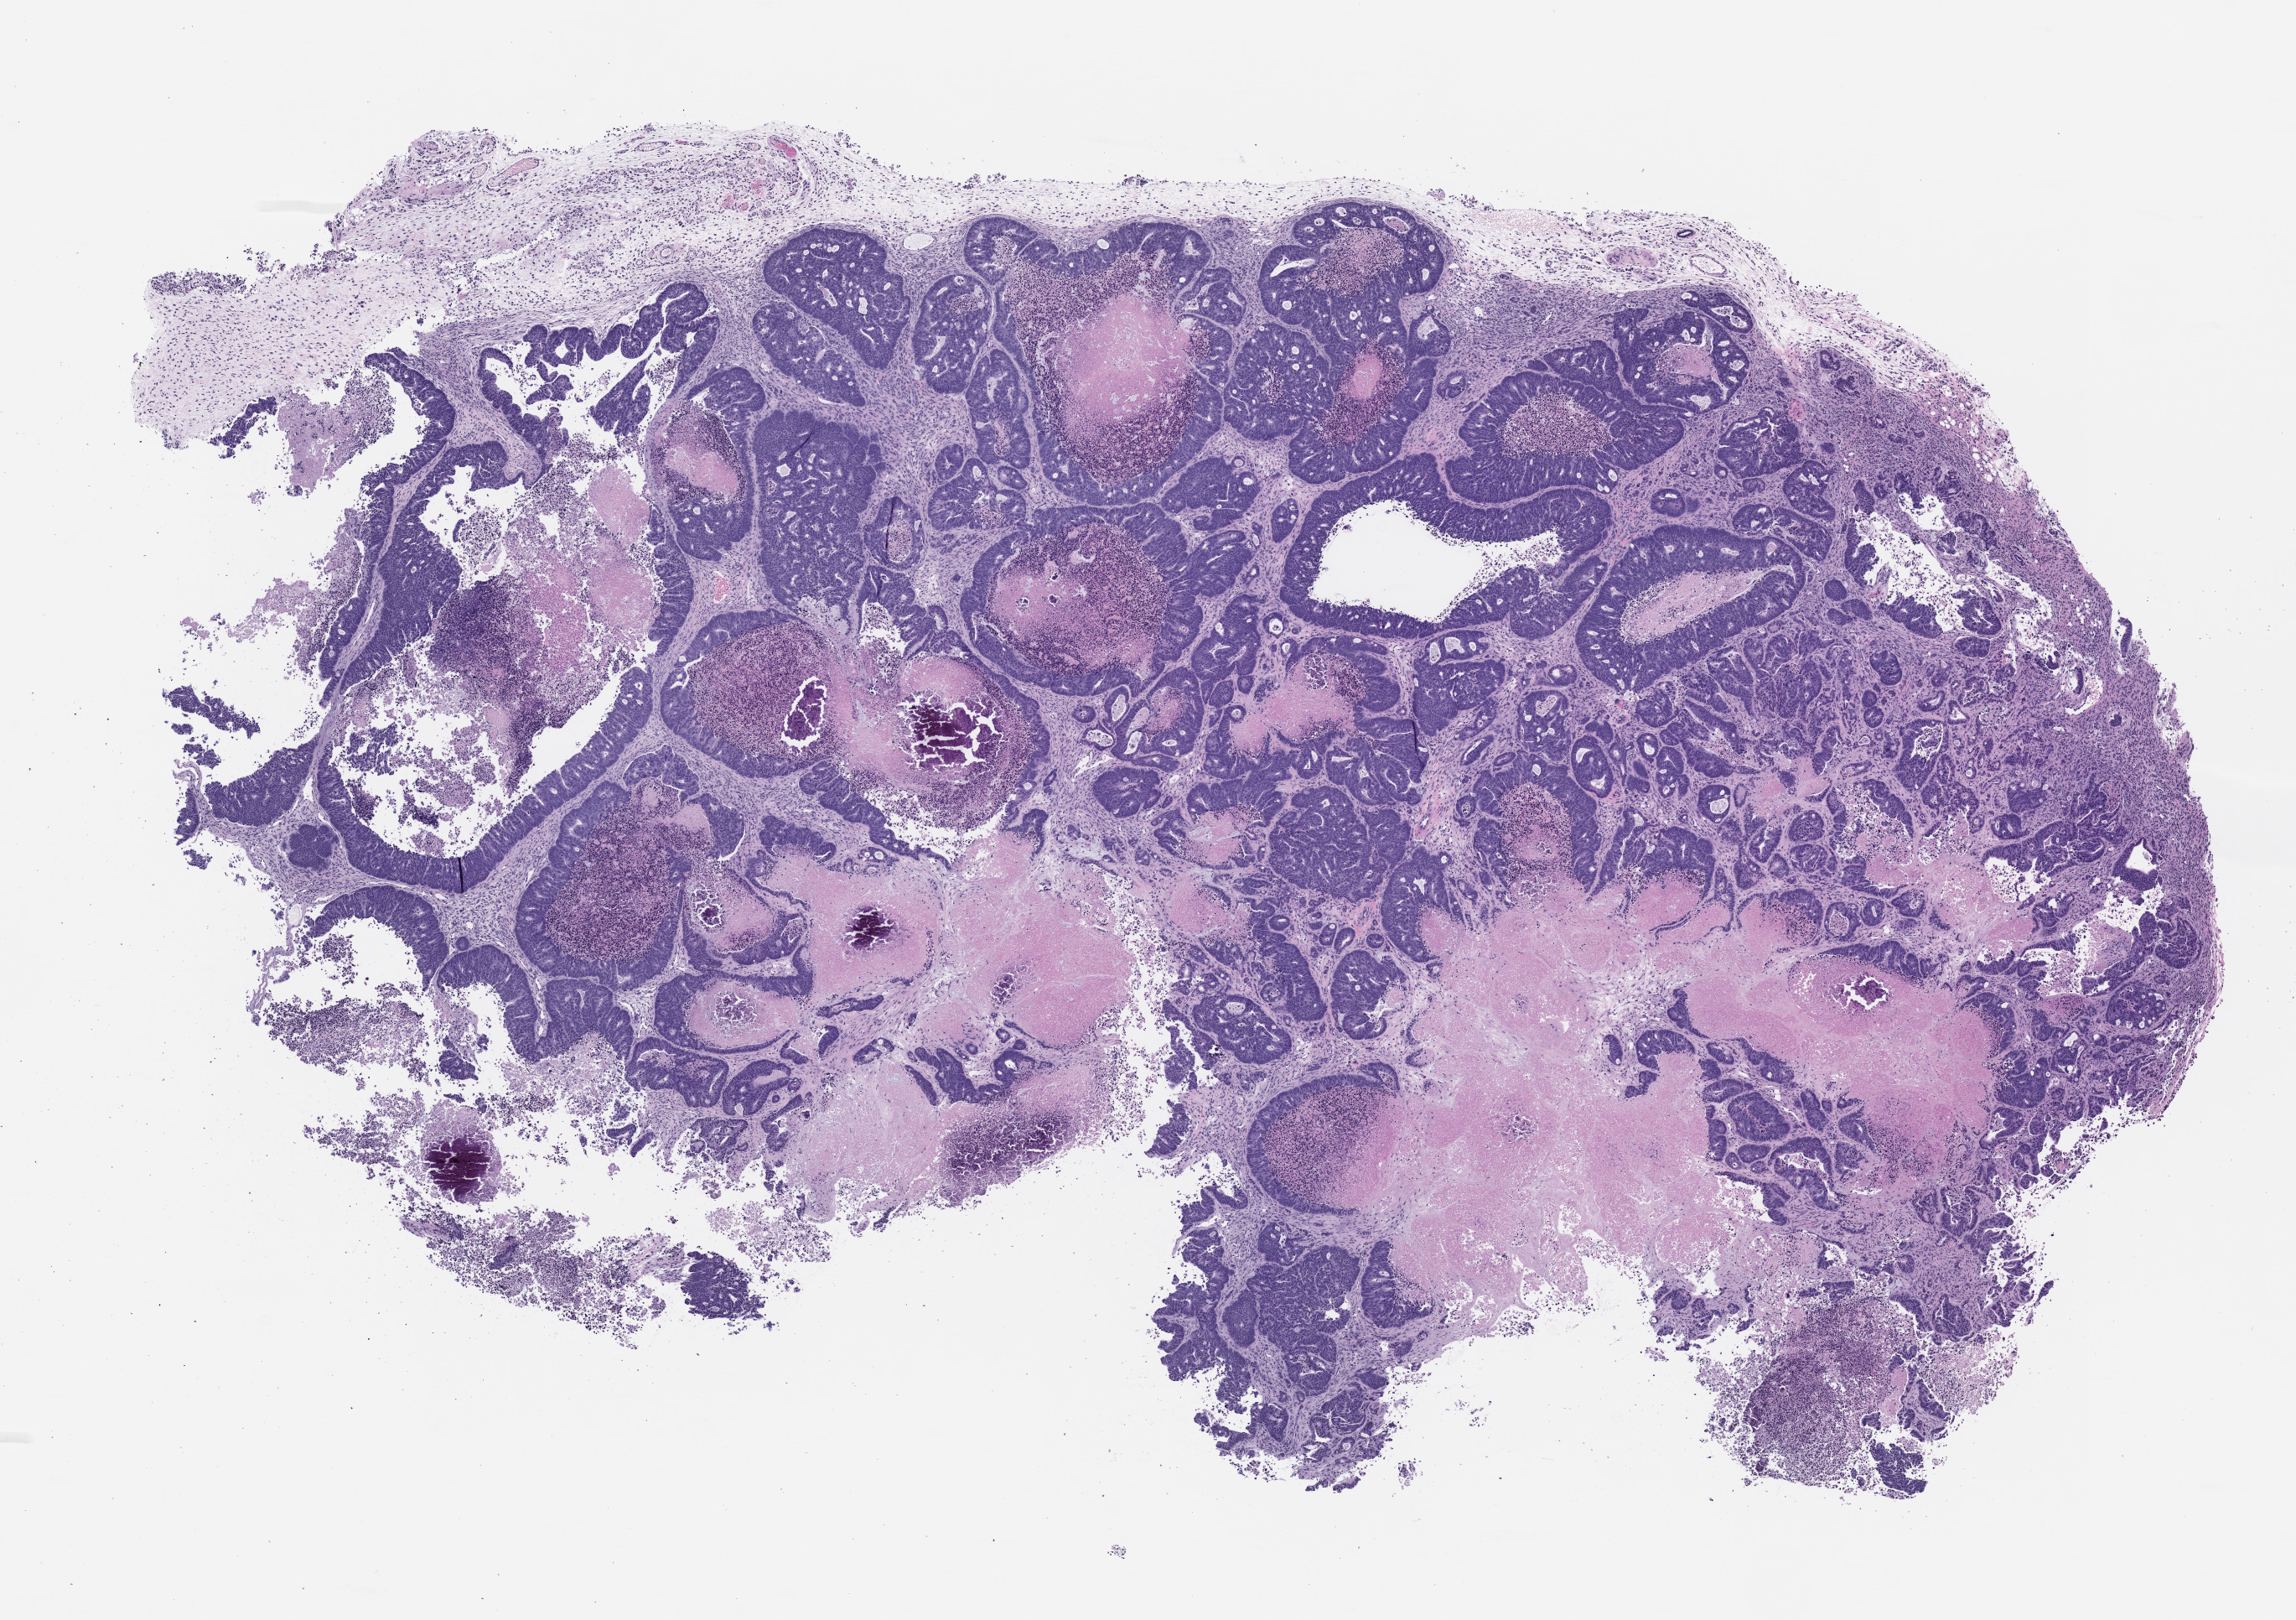
Whole-slide image, H&E: patient-derived xenograft (human tumor grown in a mouse), passage 1, shown as a low-resolution overview of the whole scanned area (about 11.0 x 7.8 mm); formalin-fixed, paraffin-embedded (FFPE) tissue; originating tumor site category: colon.
Originating patient diagnosis: Colon Adenocarcinoma.